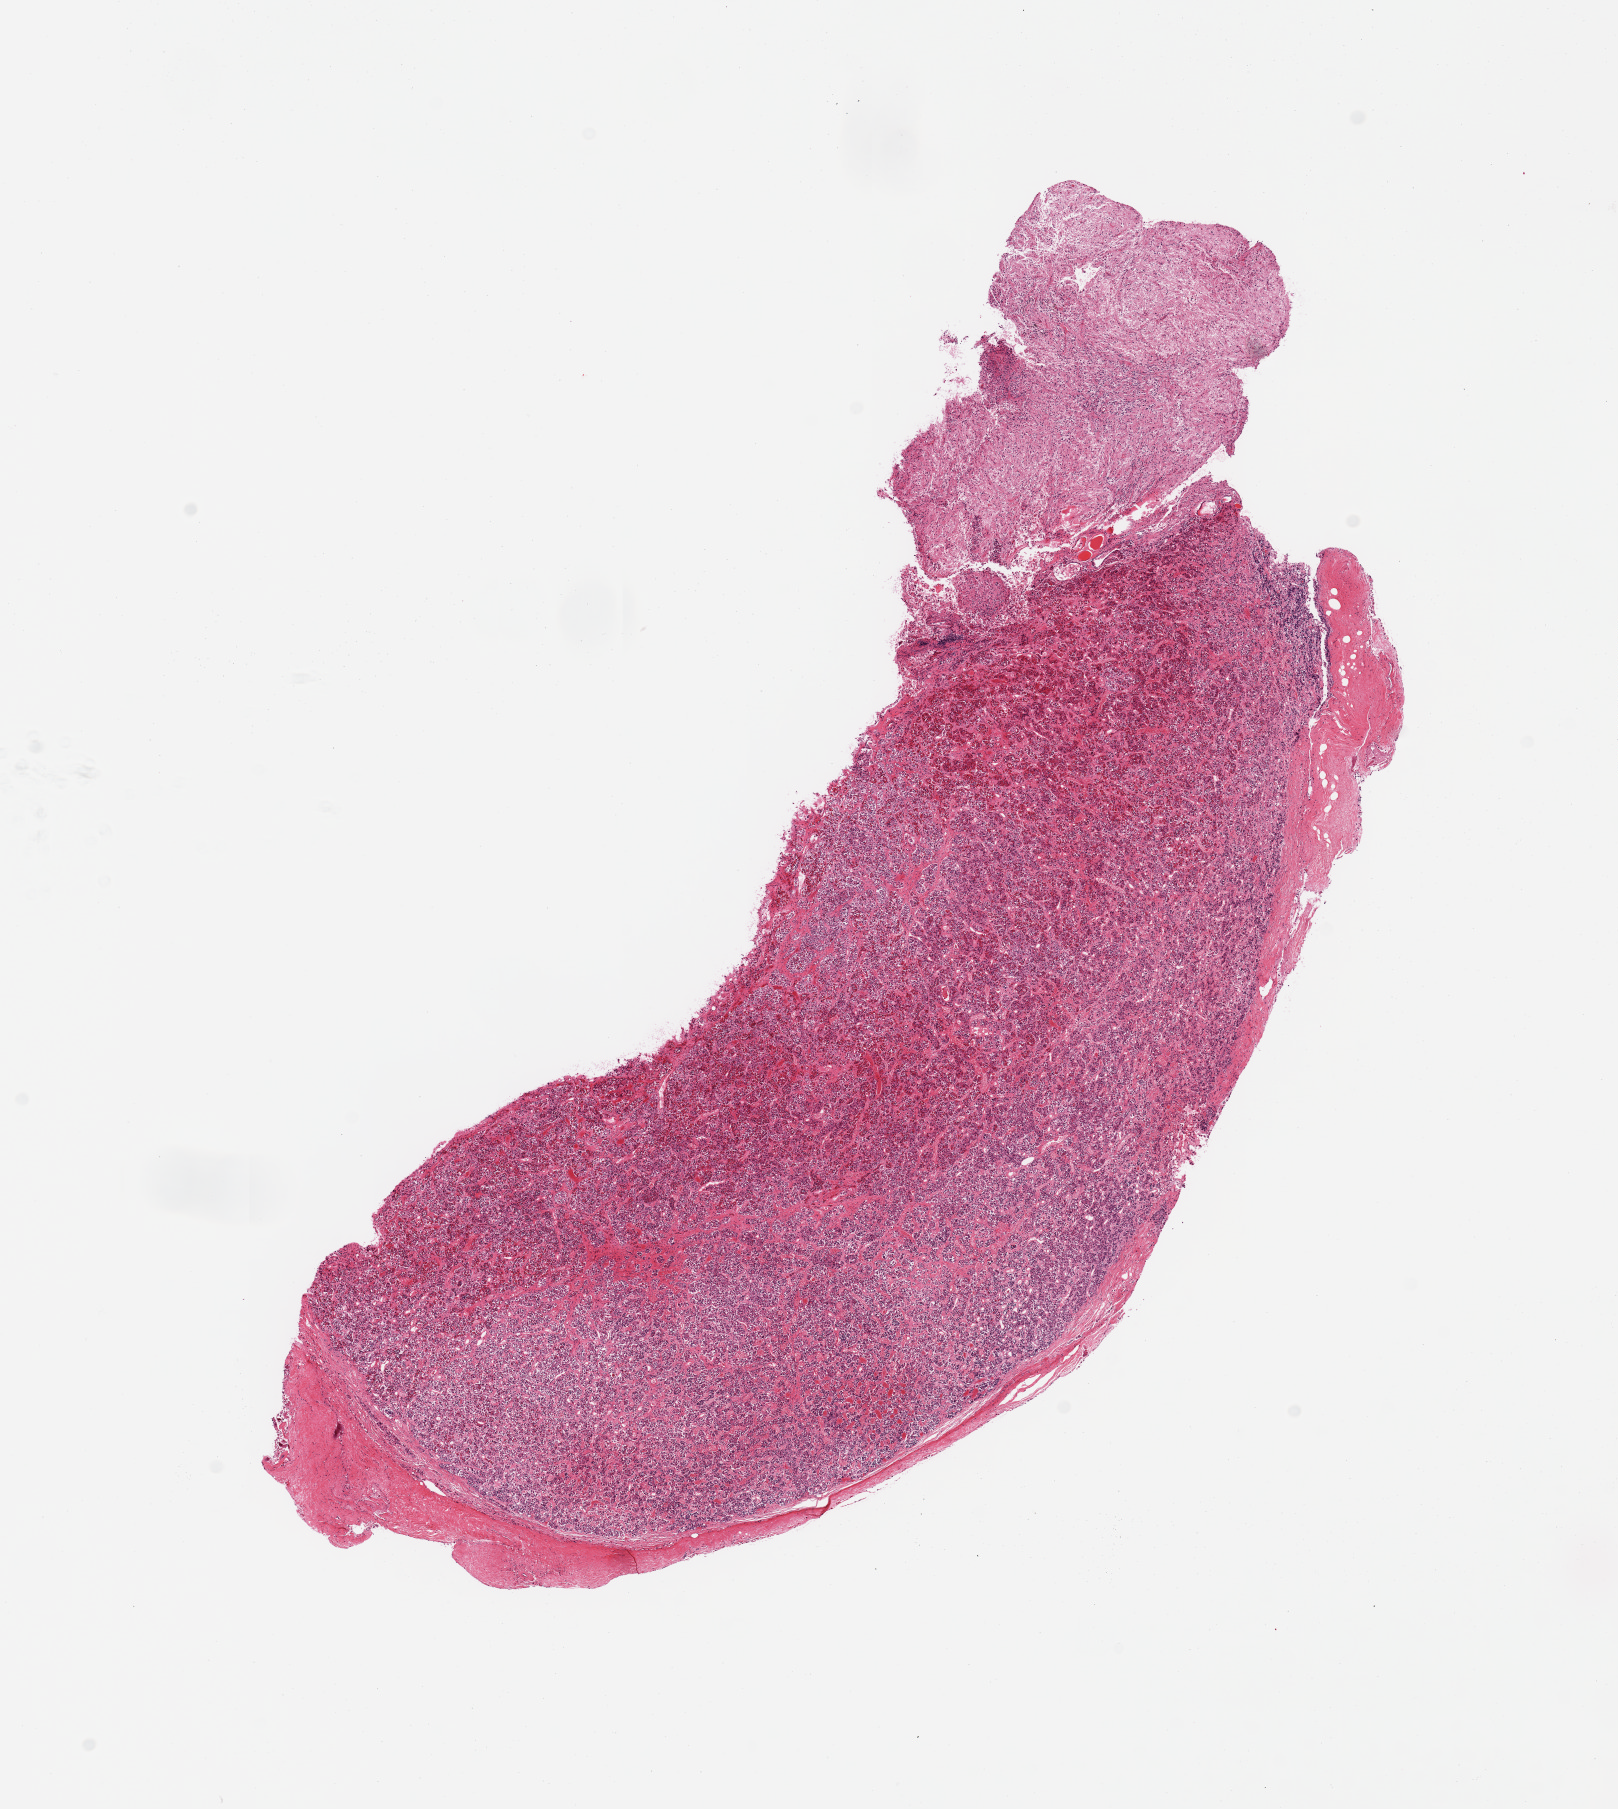
Haematoxylin and eosin whole-slide image, a low-resolution overview of the entire scanned area, about 12.8 x 14.3 mm (acquisition: 20x scan); PAXgene-fixed paraffin-embedded (PFPE) section; section of pituitary (target tissue); donor tissue sample.
Reviewer comment on this tissue sample: 1 piece; 20% posterior pituitary.